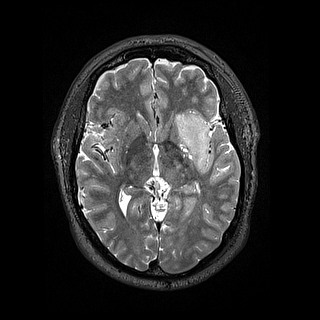
Brain MRI from a brain-tumour surgery series, one axial slice. Position 87 of 144 along the scan axis. 1.2 mm slice thickness. 320 × 320 image matrix, field of view 254 × 254 mm. From the clinical record (not read from this slice): histopathology: Astrocytoma; WHO grade: 2; IDH mutation: yes.
Structures marked on this image (expert manual segmentation):
- tumour: bounding box (x1, y1, x2, y2) in pixels: (174, 107, 211, 173)